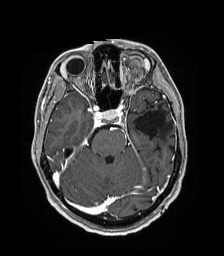
Brain MRI from a brain-tumour surgery series, one axial slice; slice 121 of 192 in the series (ordered by position); T1-weighted post-contrast; 224 × 256 image matrix, field of view 224 × 256 mm. Case-level facts recorded for this patient, not image findings: histopathology: Low grade glioma; IDH mutation: no; tumour location: Left Parieto-Occipital Intraventricular.
Annotated regions visible in this slice (outlined manually by an expert reader):
- previous resection cavity: bounding box [x1, y1, x2, y2] px = [134, 109, 165, 140]